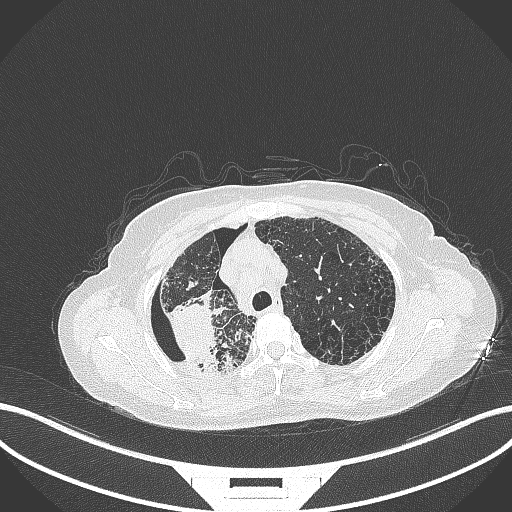
Chest CT, one axial slice; slice 276 of 408 in the series (ordered by position); reconstruction kernel B70f; lung window (W 1500 / L -600 HU); 1 mm slice thickness; 512 × 512 image matrix, field of view 400 × 400 mm. Female patient, age 64 years. From the clinical record (not read from this slice): clinical TNM (as recorded): T3 N3 M0.
Structures marked on this image (bounding box drawn by a radiologist):
- lung tumour (recorded histology: squamous cell carcinoma): box from (x=156, y=298) to (x=224, y=369) px